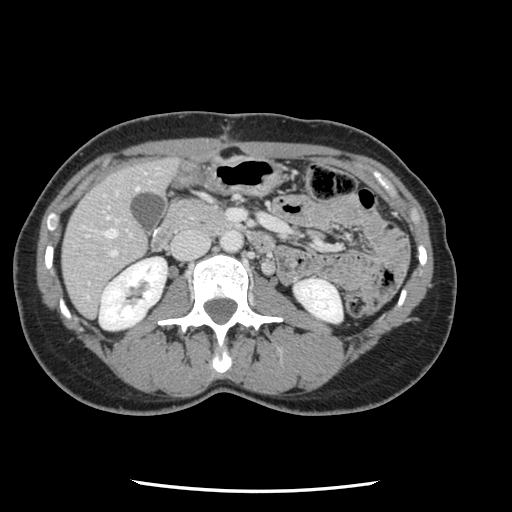
Contrast-enhanced abdominal CT, one axial slice. Slice 36 of 134 in the series (ordered by position). Intravenous contrast given. Soft-tissue window (W 400 / L 40 HU). 2.5 mm slice thickness. 512 × 512 image matrix, field of view 330 × 330 mm. Female patient, age 43 years. Case-level facts recorded for this patient, not image findings: diagnosis: colorectal cancer liver metastases, imaged before liver resection; multiple liver metastases: yes; largest metastasis: 3.4 cm; disease in both lobes: yes.
Structures marked on this image (manually delineated by an expert):
- hepatic veins: box from (x=105, y=187) to (x=139, y=239) px
- liver: (x=63, y=160)–(x=177, y=316)
- planned liver remnant (the part of the liver to remain after resection): (x=63, y=160)–(x=178, y=317)
- portal vein (with intrahepatic branches): (x=81, y=209)–(x=277, y=257)